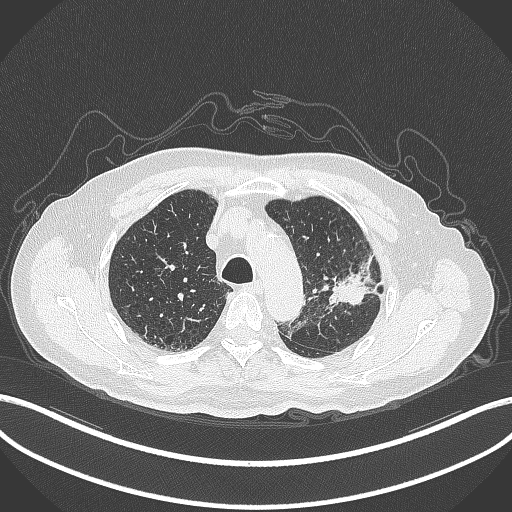
Chest CT, one axial slice; position 227 of 331 along the scan axis; 120 kVp; lung window (W 1500 / L -600 HU); 1 mm slice thickness; 512 × 512 image matrix, field of view 400 × 400 mm. Male patient, age 79 years. Case-level facts recorded for this patient, not image findings: clinical TNM (as recorded): T2a N1 M1.
Outlined on this slice (bounding box drawn by a radiologist):
- lung tumour (recorded histology: adenocarcinoma): bounding box <327,257,389,315> (left, top, right, bottom; pixels)